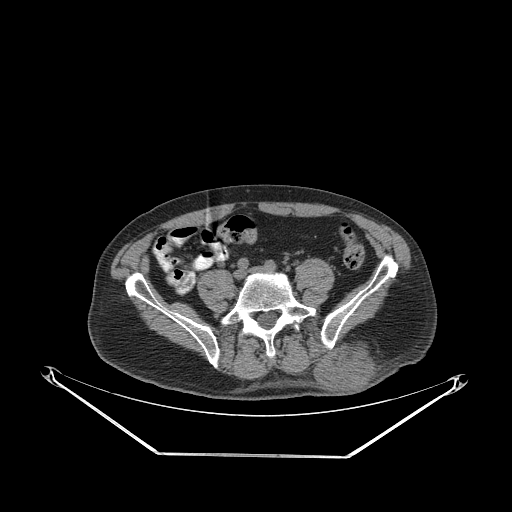
CT of an extremity soft-tissue mass (from a PET/CT study), one axial slice. Slice 87 of 267 in the series (ordered by position). Reconstruction kernel STANDARD. 140 kVp. Soft-tissue window (W 400 / L 40 HU). 512 × 512 image matrix, field of view 500 × 500 mm. Male patient. From the clinical record (not read from this slice): histological type: leiomyosarcoma; grade: intermediate; site of the primary tumour: left pelvis.
Annotated regions visible in this slice (expert contour drawn on MRI and transferred to this co-registered scan by the dataset authors):
- gross tumour volume (mass): bounding box <315,342,378,391> (left, top, right, bottom; pixels)